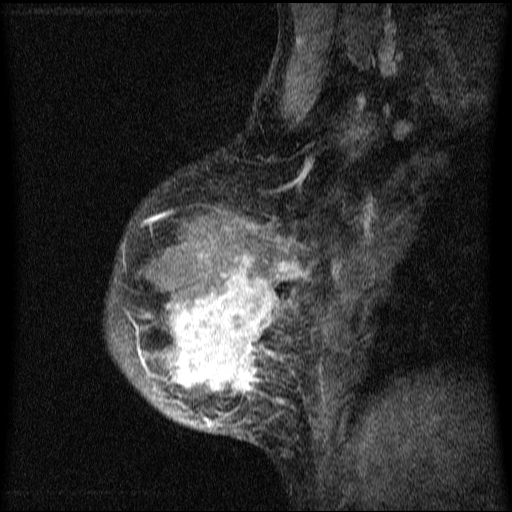
Breast MRI (dynamic contrast-enhanced), one sagittal slice. Slice 50 of 64 in the series (ordered by position). Dynamic contrast-enhanced series, image 2 of 4 at this slice position (ordered by acquisition). 1.5 T. TE 4.2 ms, TR 9.1 ms. 2 mm slice thickness. 512 × 512 image matrix, field of view 180 × 180 mm. Patient: female, 33 years.
Annotated regions visible in this slice (semi-automatic segmentation, software-assisted and operator-edited):
- analysis volume of interest (the breast-tissue region the enhancement analysis was run in; not a lesion): bounding box (x1, y1, x2, y2) in pixels: (108, 154, 336, 447)
- tumour enhancement mask (voxels above the 70 % enhancement threshold inside the analysis volume of interest): (129, 183, 302, 428)